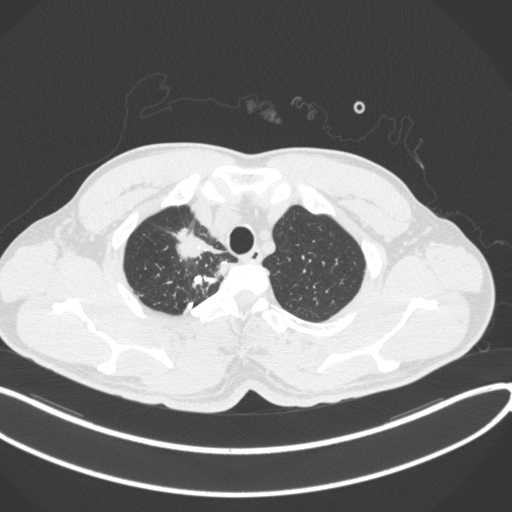
Chest CT, one axial slice. Slice 327 of 391 in the series (ordered by position). Reconstruction kernel B31f. 120 kVp. Lung window (W 1500 / L -600 HU). 512 × 512 image matrix. Patient: male, 48 years. Case-level facts recorded for this patient, not image findings: clinical TNM (as recorded): T1c N1 M1.
Annotated regions visible in this slice (bounding box drawn by a radiologist):
- lung tumour (recorded histology: adenocarcinoma): bounding box [x1, y1, x2, y2] px = [172, 221, 225, 262]